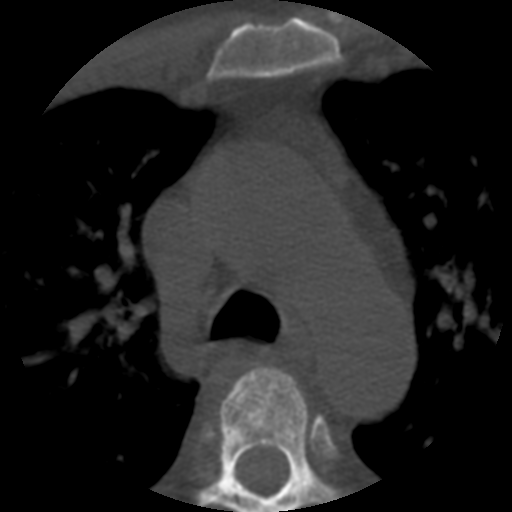
CT including the spine, one axial slice; slice 396 of 508 in the series (ordered by position); reconstruction kernel STANDARD; bone window (W 1800 / L 400 HU); 1.25 mm slice thickness; 512 × 512 image matrix, field of view 160 × 160 mm. Patient age 57 years. Case-level facts recorded for this patient, not image findings: primary cancer: prostate.
Structures marked on this image (semi-automatically segmented with operator editing):
- T3 vertebra: bounding box <230,366,297,397> (left, top, right, bottom; pixels)
- T4 vertebra: <199,377,335,512>
- T5 vertebra: <235,479,245,488>